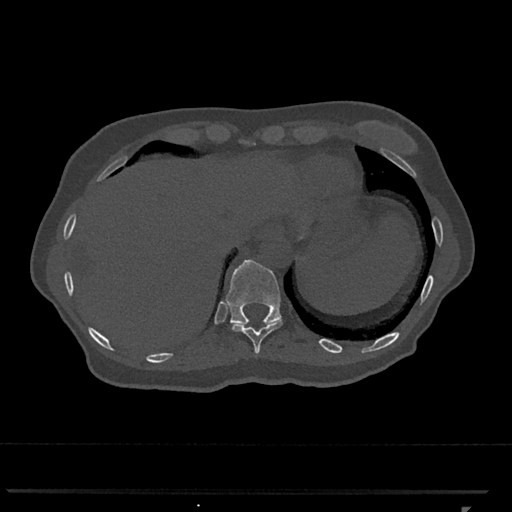
CT including the spine, one axial slice; position 544 of 793 along the scan axis; reconstruction kernel Br40s/3; 120 kVp; bone window (W 1800 / L 400 HU); 0.5 mm slice thickness; 512 × 512 image matrix. Female patient, age 62 years. From the clinical record (not read from this slice): primary cancer: renal.
Annotated regions visible in this slice (semi-automatic segmentation, software-assisted and operator-edited):
- T10 vertebra: box from (x=229, y=322) to (x=282, y=354) px
- T11 vertebra: (x=226, y=259)–(x=282, y=327)